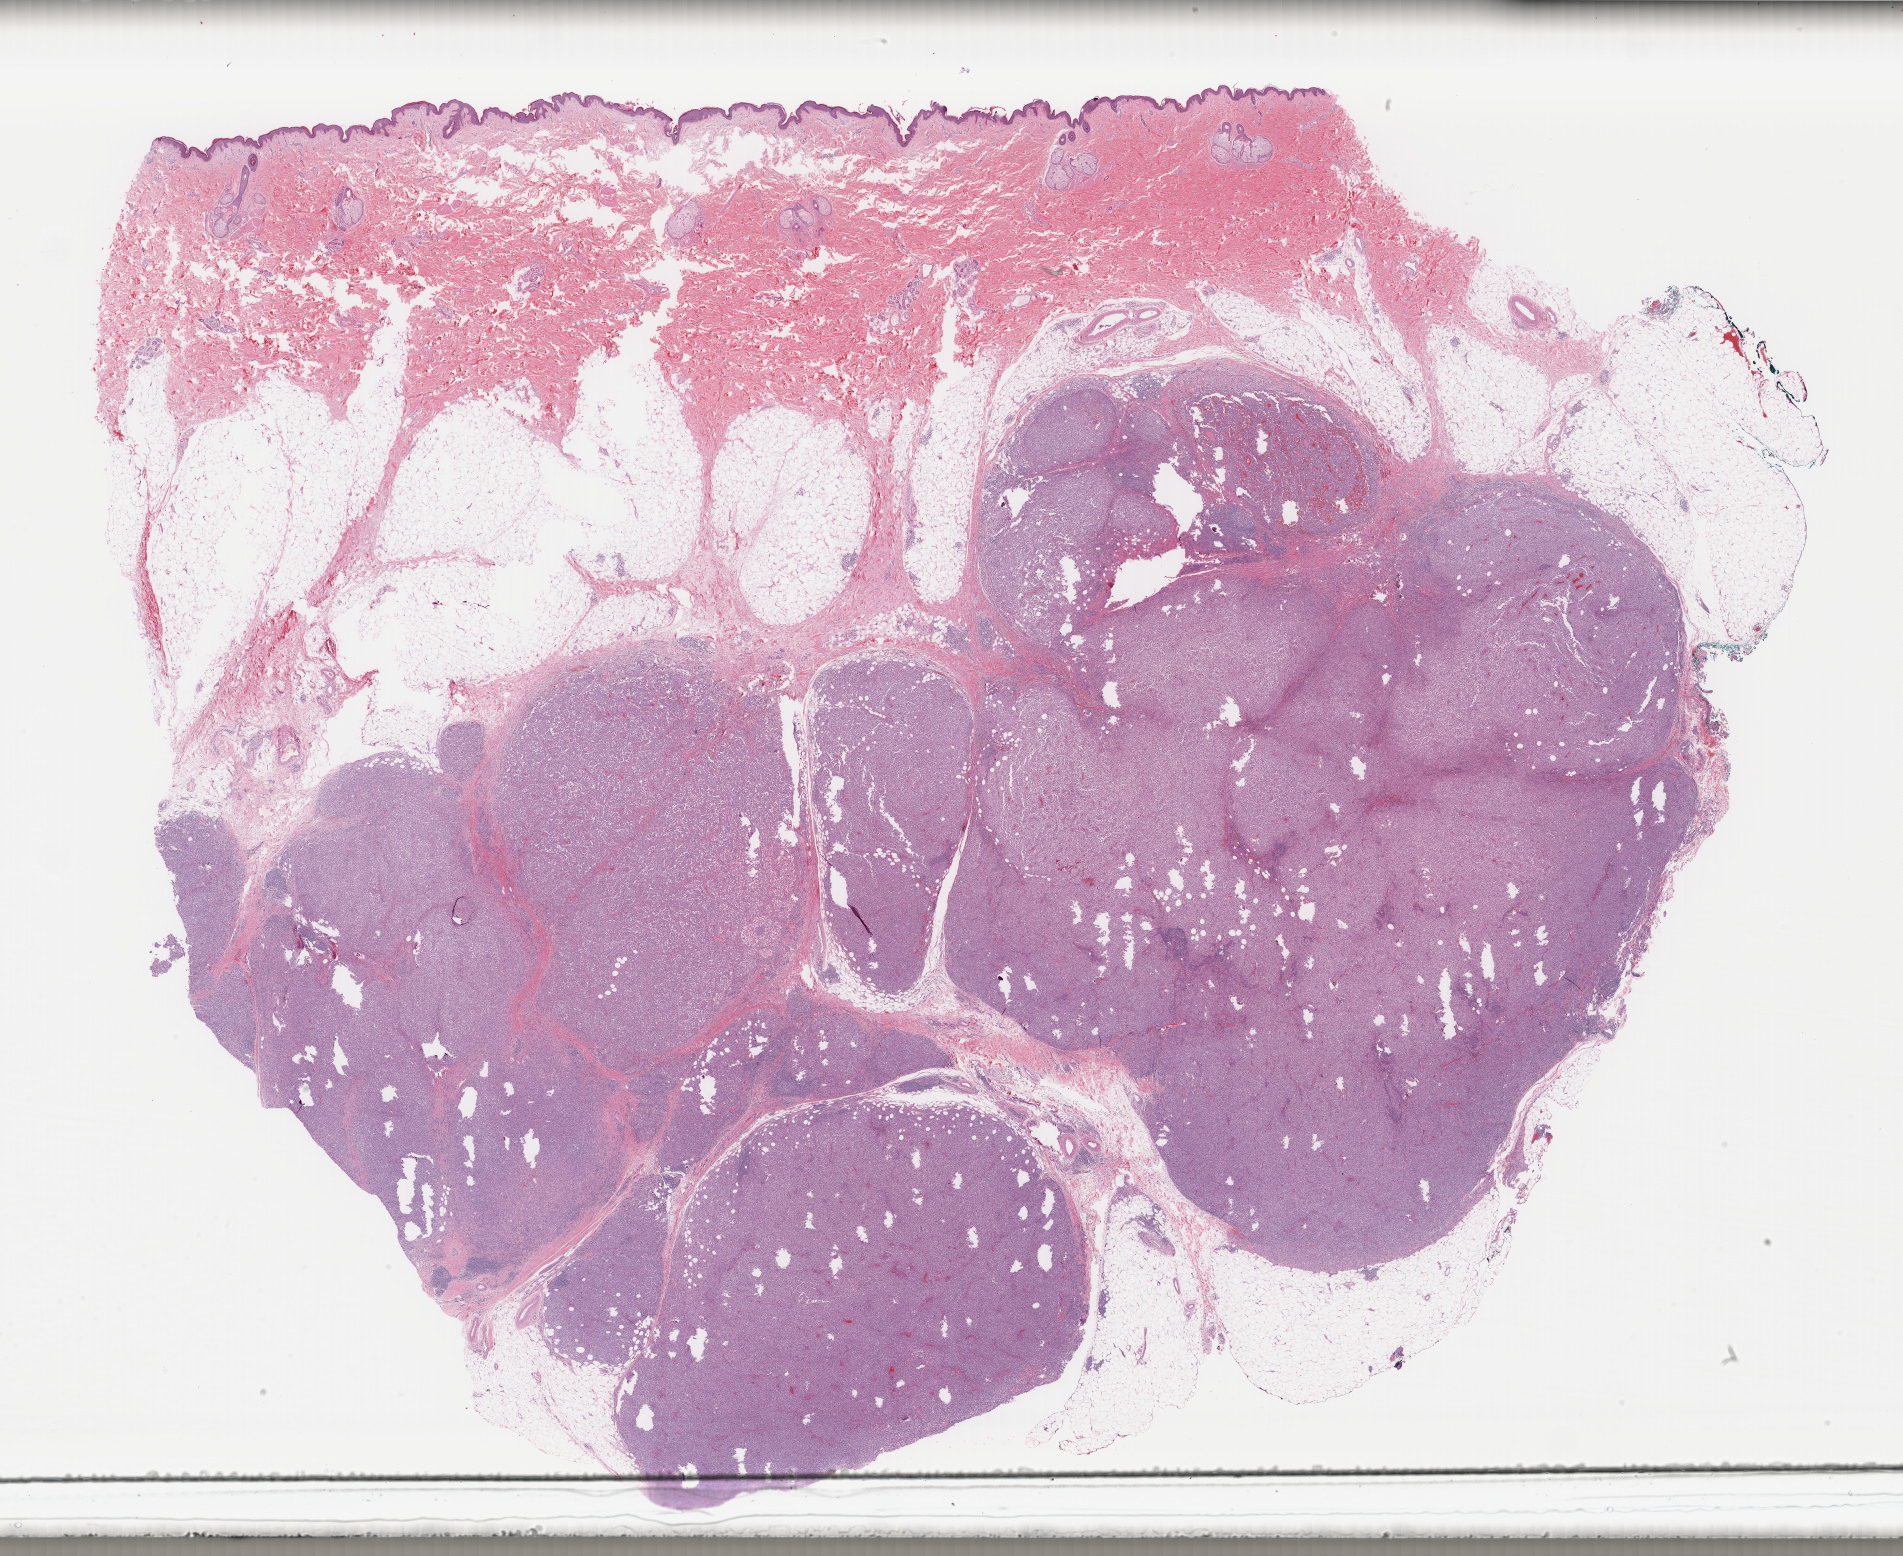
Whole-slide histology image, H&E-stained, whole scanned area (about 30.2 x 24.7 mm) shown as a low-resolution overview; formalin-fixed paraffin-embedded (FFPE) diagnostic section; skin, primary tumour sample. Male, age 40 years at initial diagnosis.
Histologic diagnosis: Malignant melanoma, NOS.